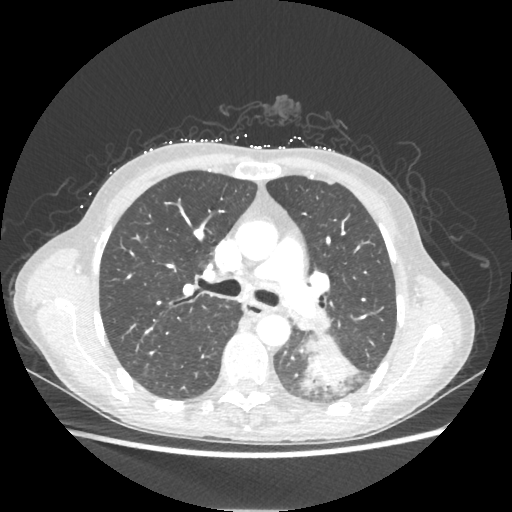
Chest CT, one axial slice; slice 137 of 221 in the series (ordered by position); reconstruction kernel STANDARD; 80 kVp; lung window (W 1500 / L -600 HU); 512 × 512 image matrix, field of view 360 × 360 mm. Female patient, age 53 years. Case-level facts recorded for this patient, not image findings: clinical TNM (as recorded): T3 N0 M0.
Outlined on this slice (rectangle marked by the reading radiologist):
- lung tumour (recorded histology: adenocarcinoma): bounding box <305,339,357,392> (left, top, right, bottom; pixels)